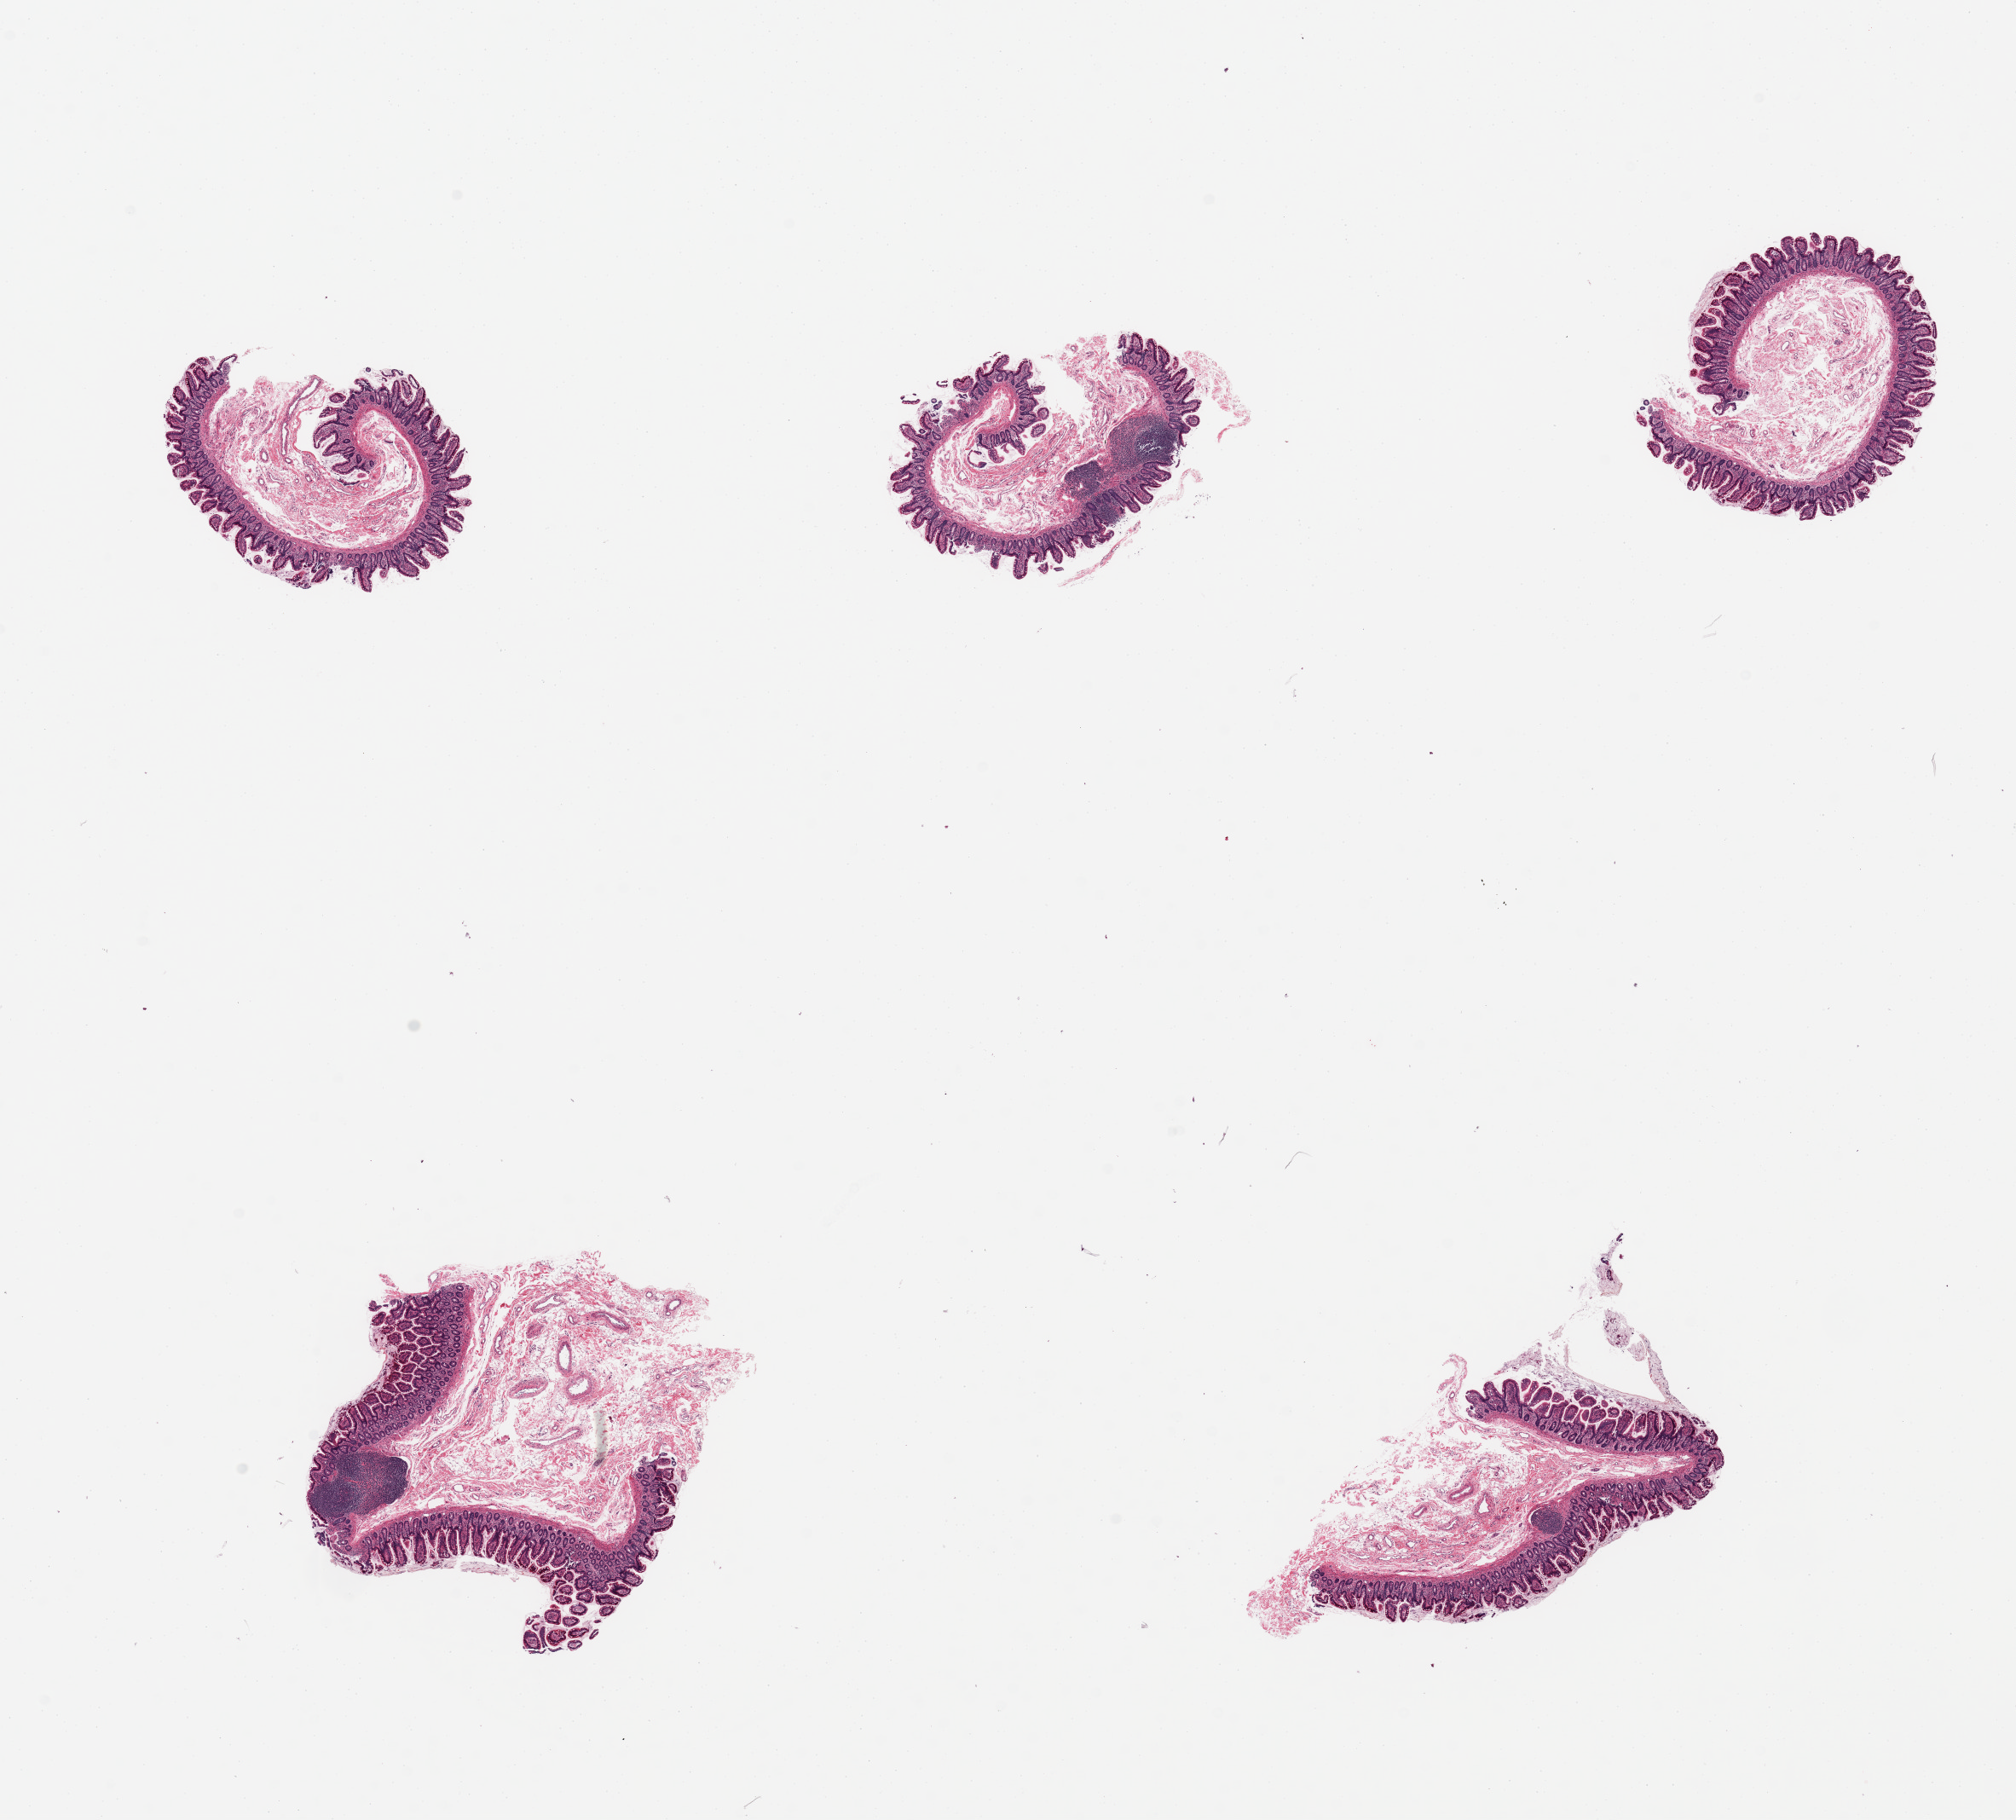
Whole-slide image, H&E stain, brightfield — shown as a low-resolution overview of the whole scanned area (about 18.7 x 16.9 mm); PAXgene-fixed, paraffin-embedded tissue; sampled site (target tissue): ileum; donor tissue sample. Donor sex: female.
* review note (as recorded): 5 pieces, few lymphoid aggregates